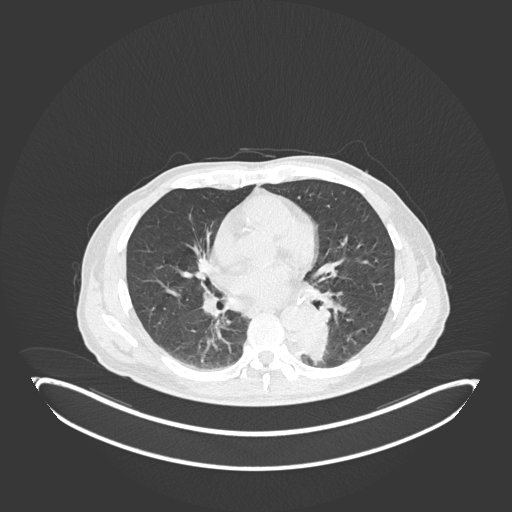
Chest CT, one axial slice. Position 94 of 251 along the scan axis. 120 kVp. Lung window (W 1500 / L -600 HU). 1 mm slice thickness. 512 × 512 image matrix, field of view 500 × 500 mm. Patient: male, 72 years. Case-level facts recorded for this patient, not image findings: clinical TNM (as recorded): T2b N0 M1.
Annotated regions visible in this slice (bounding box drawn by a radiologist):
- lung tumour (recorded histology: adenocarcinoma): box from (x=287, y=321) to (x=330, y=364) px